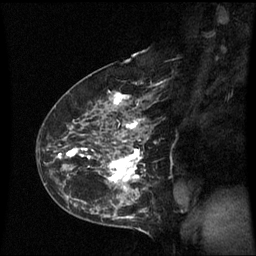
Breast MRI (dynamic contrast-enhanced), one sagittal slice; position 39 of 60 along the scan axis; dynamic contrast-enhanced series, image 2 of 3 at this slice position (ordered by acquisition); 1.5 T; TE 4.2 ms, TR 8.9 ms; 256 × 256 image matrix, field of view 210 × 210 mm. Female patient, age 43 years. Case-level facts recorded for this patient, not image findings: setting: breast cancer imaged before/during neoadjuvant chemotherapy; receptor status: HER2-positive.
Outlined on this slice (semi-automatically segmented with operator editing):
- analysis volume of interest (the breast-tissue region the enhancement analysis was run in; not a lesion): bounding box (x1, y1, x2, y2) in pixels: (56, 80, 153, 195)
- tumour enhancement mask (voxels above the 70 % enhancement threshold inside the analysis volume of interest): (58, 93, 143, 191)